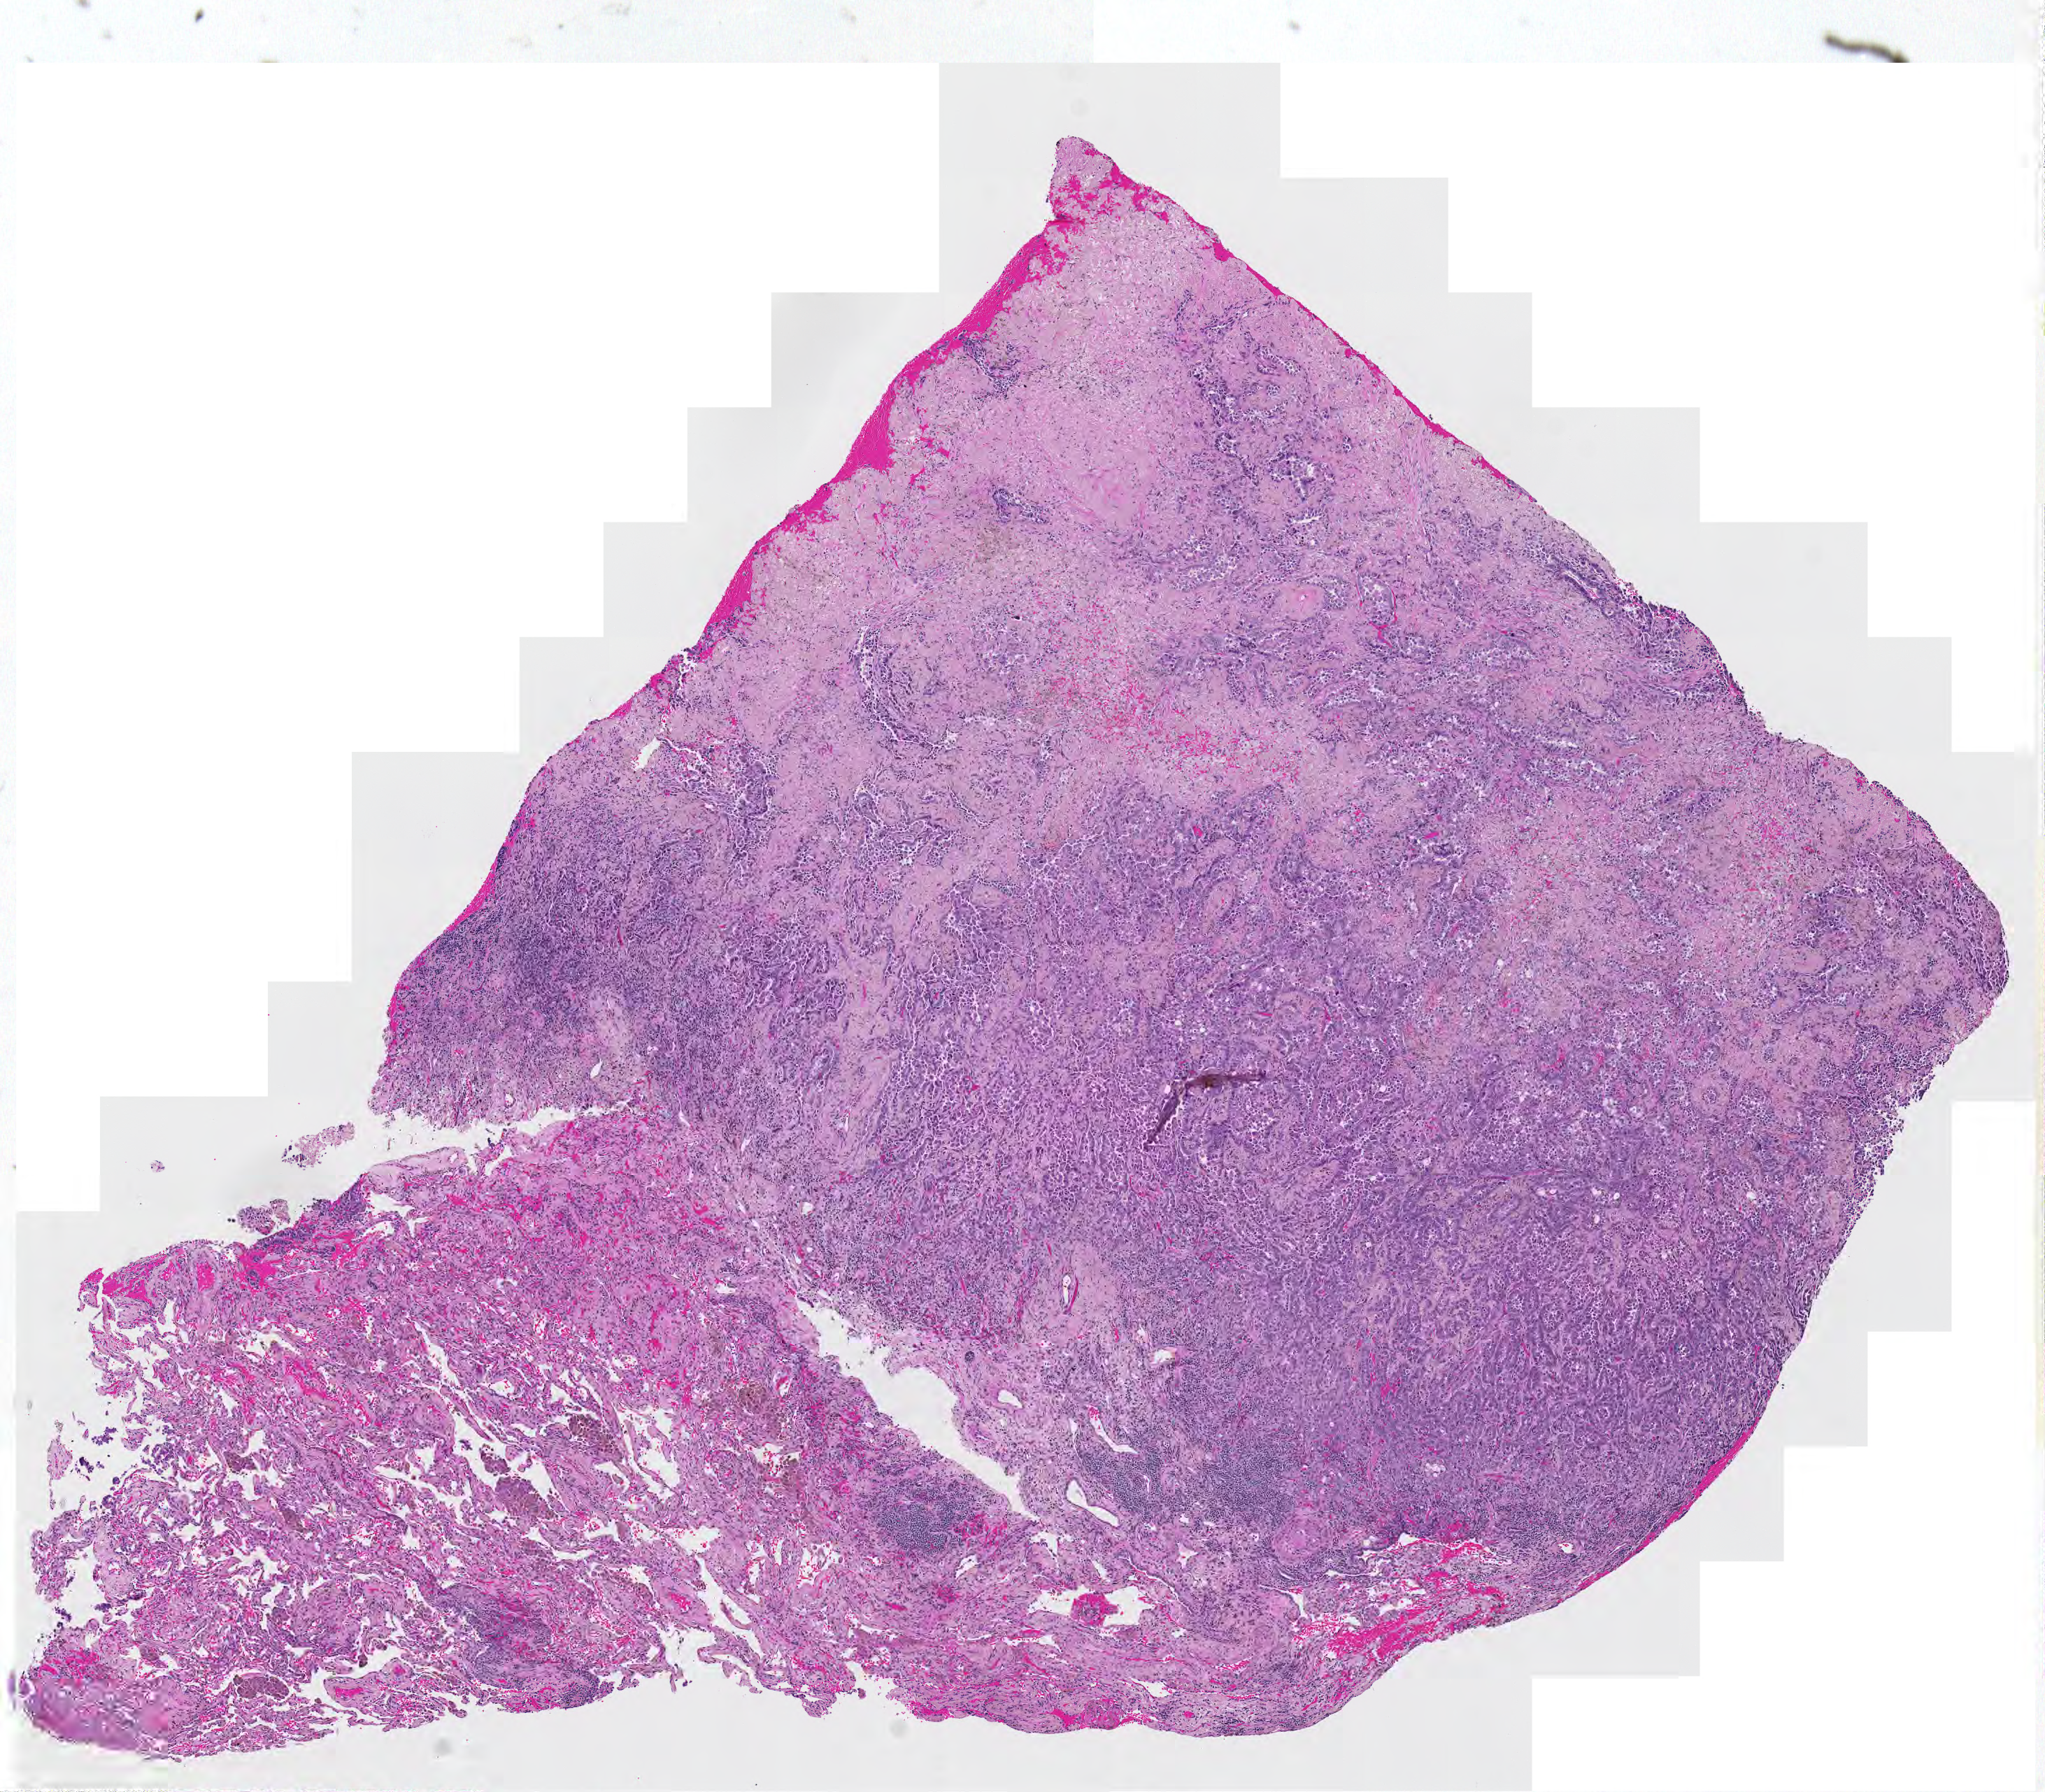
Whole-slide histology image, H&E — a low-resolution overview of the entire scanned area, about 7.5 x 6.6 mm; tumour tissue sample, sampled site: lung. 68-year-old female patient. Histologic grade: G2 (moderately differentiated). Composition of this section per pathologist review: tumour nuclei 65%, necrosis 2%.
Primary tumour site (as recorded): right upper lobe. AJCC pathologic stage: IA. Diagnosis: Adenocarcinoma, NOS.